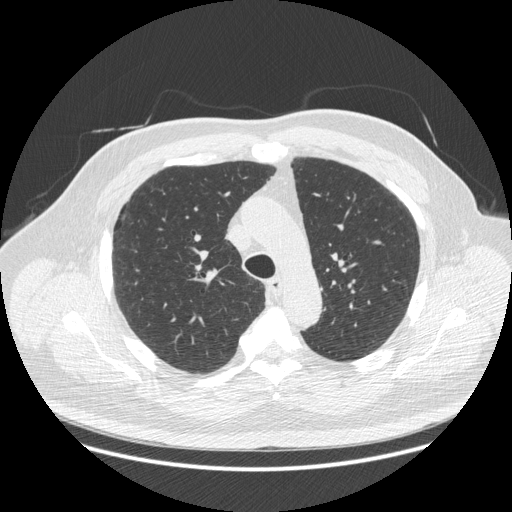
Chest CT (low-dose screening protocol), one axial image. Baseline annual screen. Lung window (W 1500 / L -600 HU). 1.25 mm slice thickness. Slice 80 of 266 in the series. 512 × 512 image matrix. Male, age 66 years at enrolment. Current smoker at enrolment.
- Expert reader's lesion annotation, bounding box (x1, y1, x2, y2) in pixels: (111, 205, 149, 235).
- Screening reader's record for this exam: no non-calcified nodule ≥4 mm recorded.
- Official screen result: negative screen, no significant abnormalities.
- Later outcome: lung cancer diagnosed 742 days after this screen (after the third annual screen) — non-small cell carcinoma, right upper lobe, stage IV (AJCC 6th edition), 50 mm at pathology.